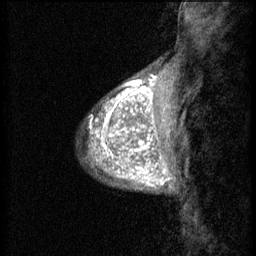
Breast MRI (dynamic contrast-enhanced), one sagittal slice. Position 12 of 60 along the scan axis. 3 images stored at this slice position (order not interpretable as contrast timing). 1.5 T. TE 4.2 ms, TR 8.2 ms. 2 mm slice thickness. 256 × 256 image matrix, field of view 180 × 180 mm. Patient: female, 38 years.
Annotated regions visible in this slice (semi-automatic segmentation, software-assisted and operator-edited):
- analysis volume of interest (the breast-tissue region the enhancement analysis was run in; not a lesion): bounding box [x1, y1, x2, y2] px = [95, 106, 157, 171]
- tumour enhancement mask (voxels above the 70 % enhancement threshold inside the analysis volume of interest): [95, 106, 157, 171]